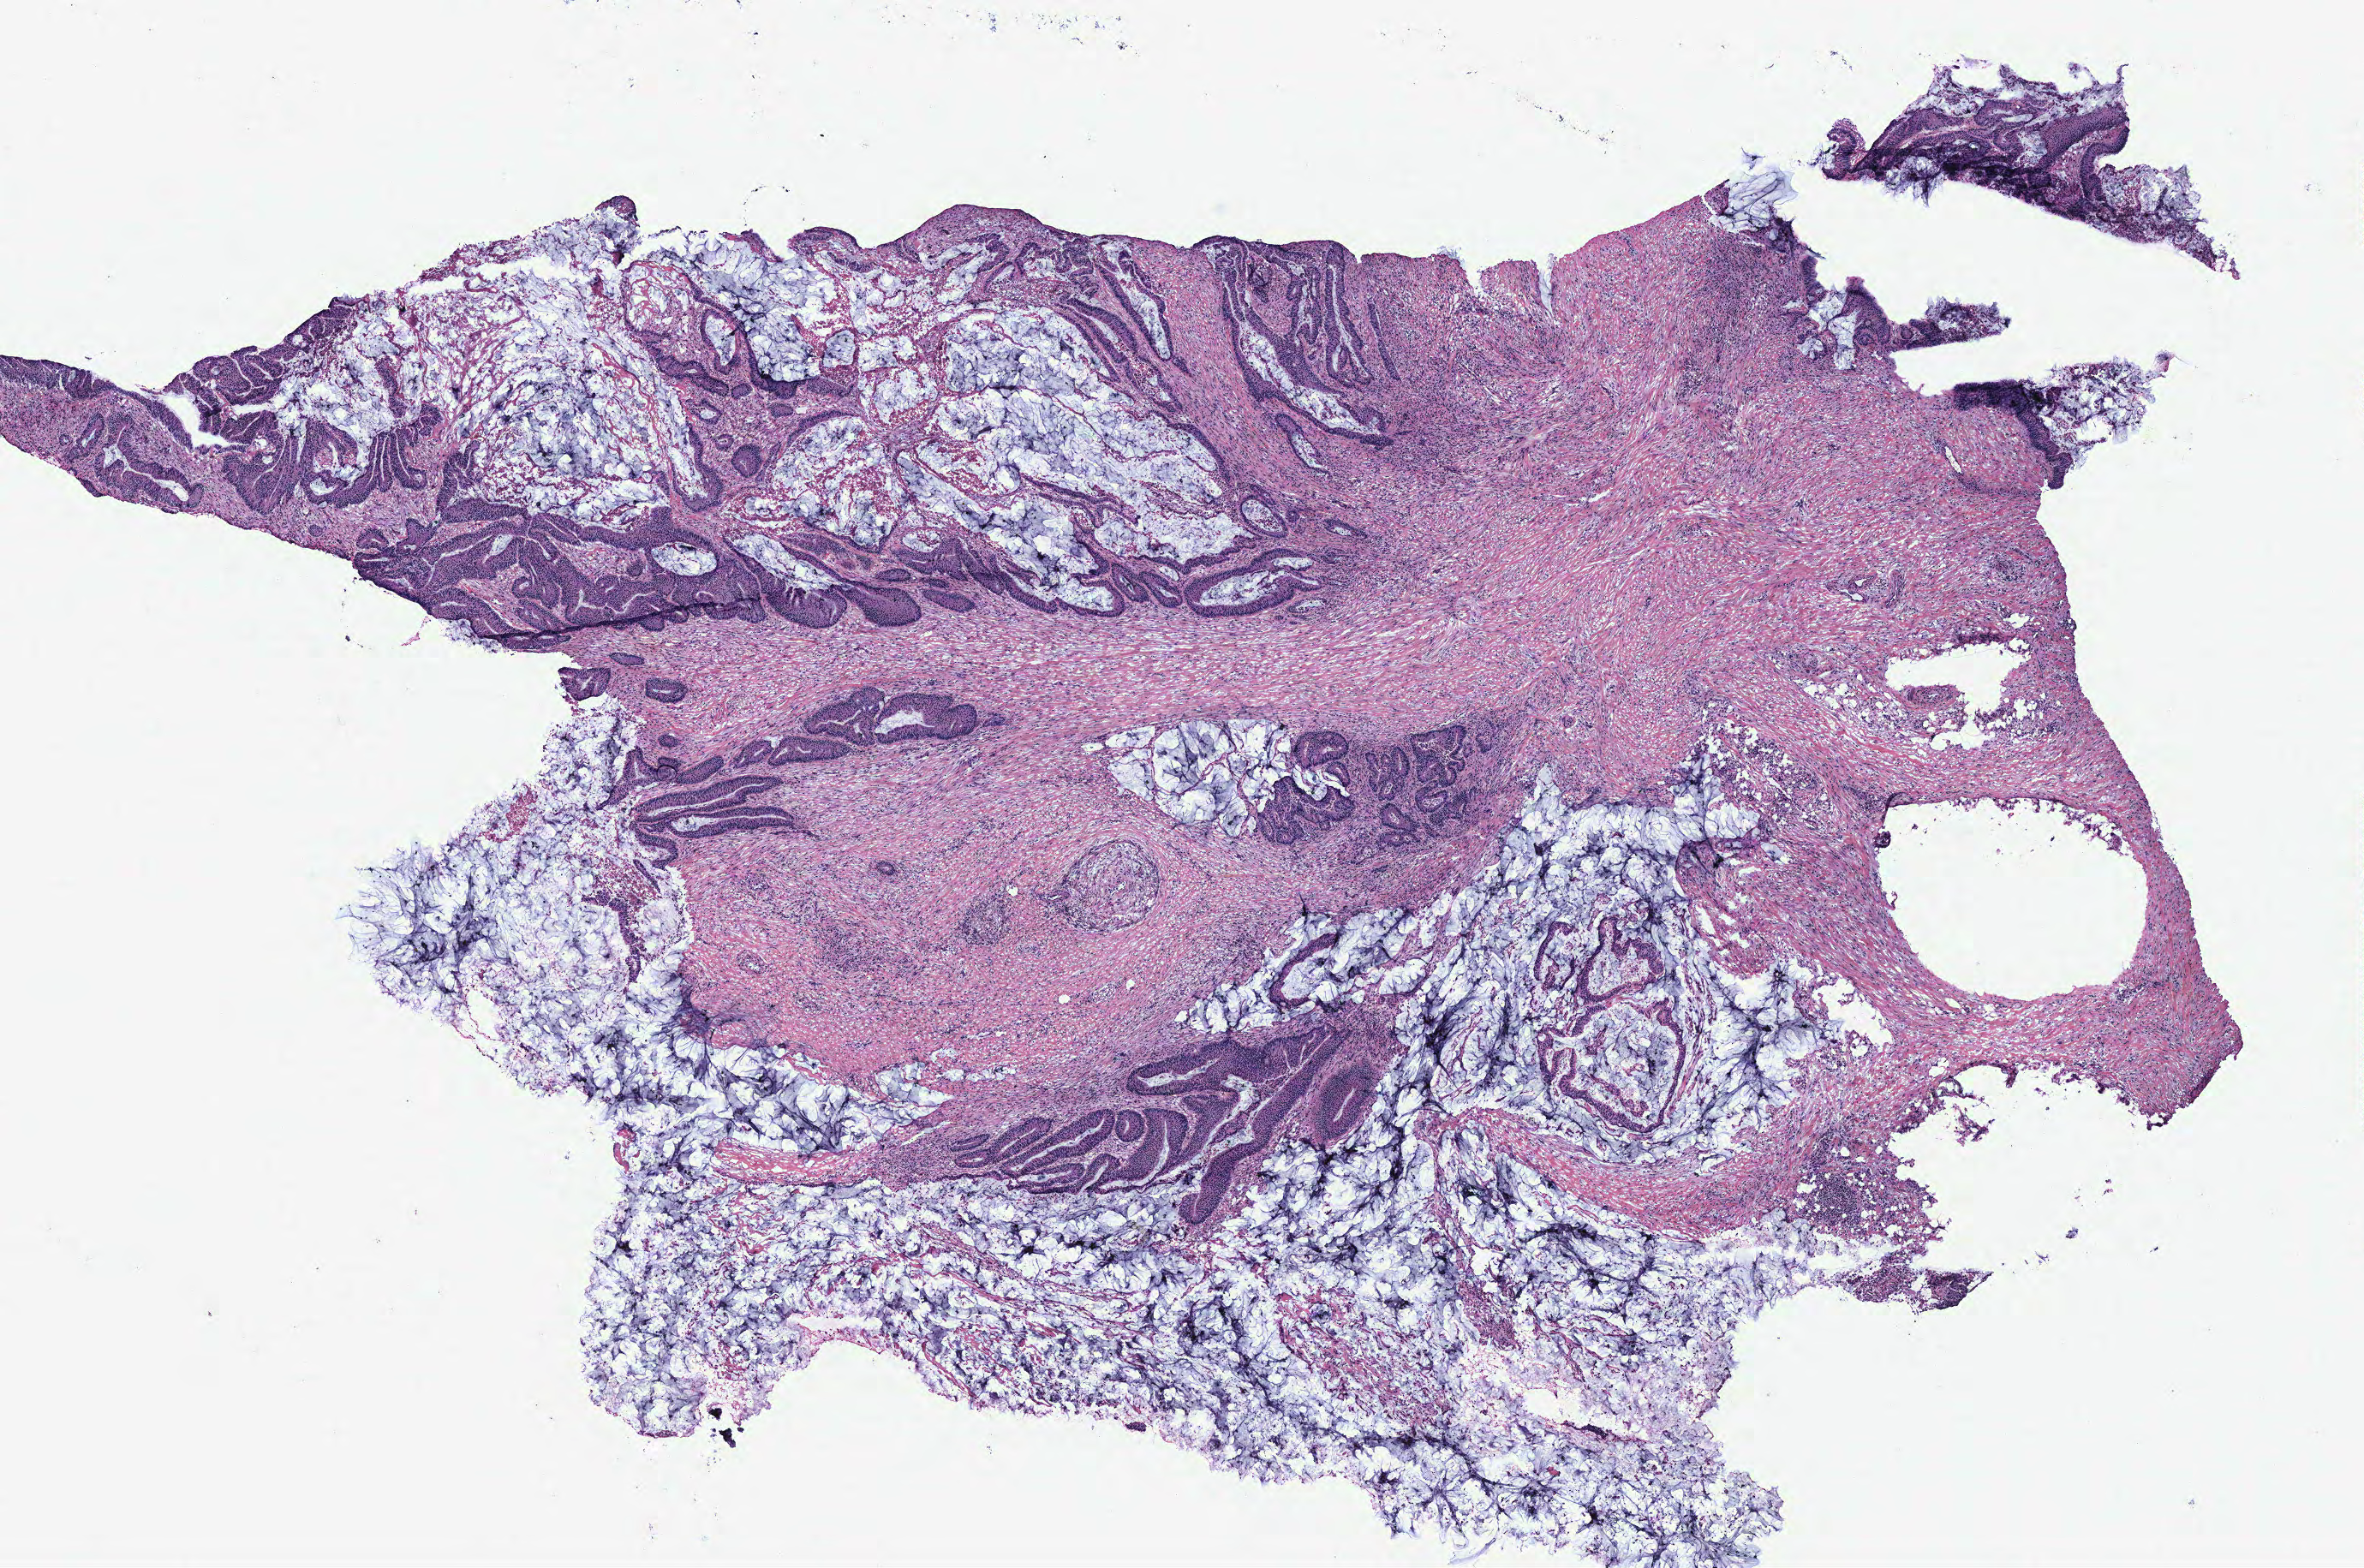
Whole-slide histology image, H&E-stained, shown as a low-resolution overview of the whole scanned area (about 11.0 x 7.3 mm, from a 40x scan); colon, tumour tissue. 50-year-old male patient.
Primary tumour site (as recorded): colon. AJCC pathologic stage: IIA. Histologic diagnosis: Adenocarcinoma, NOS.